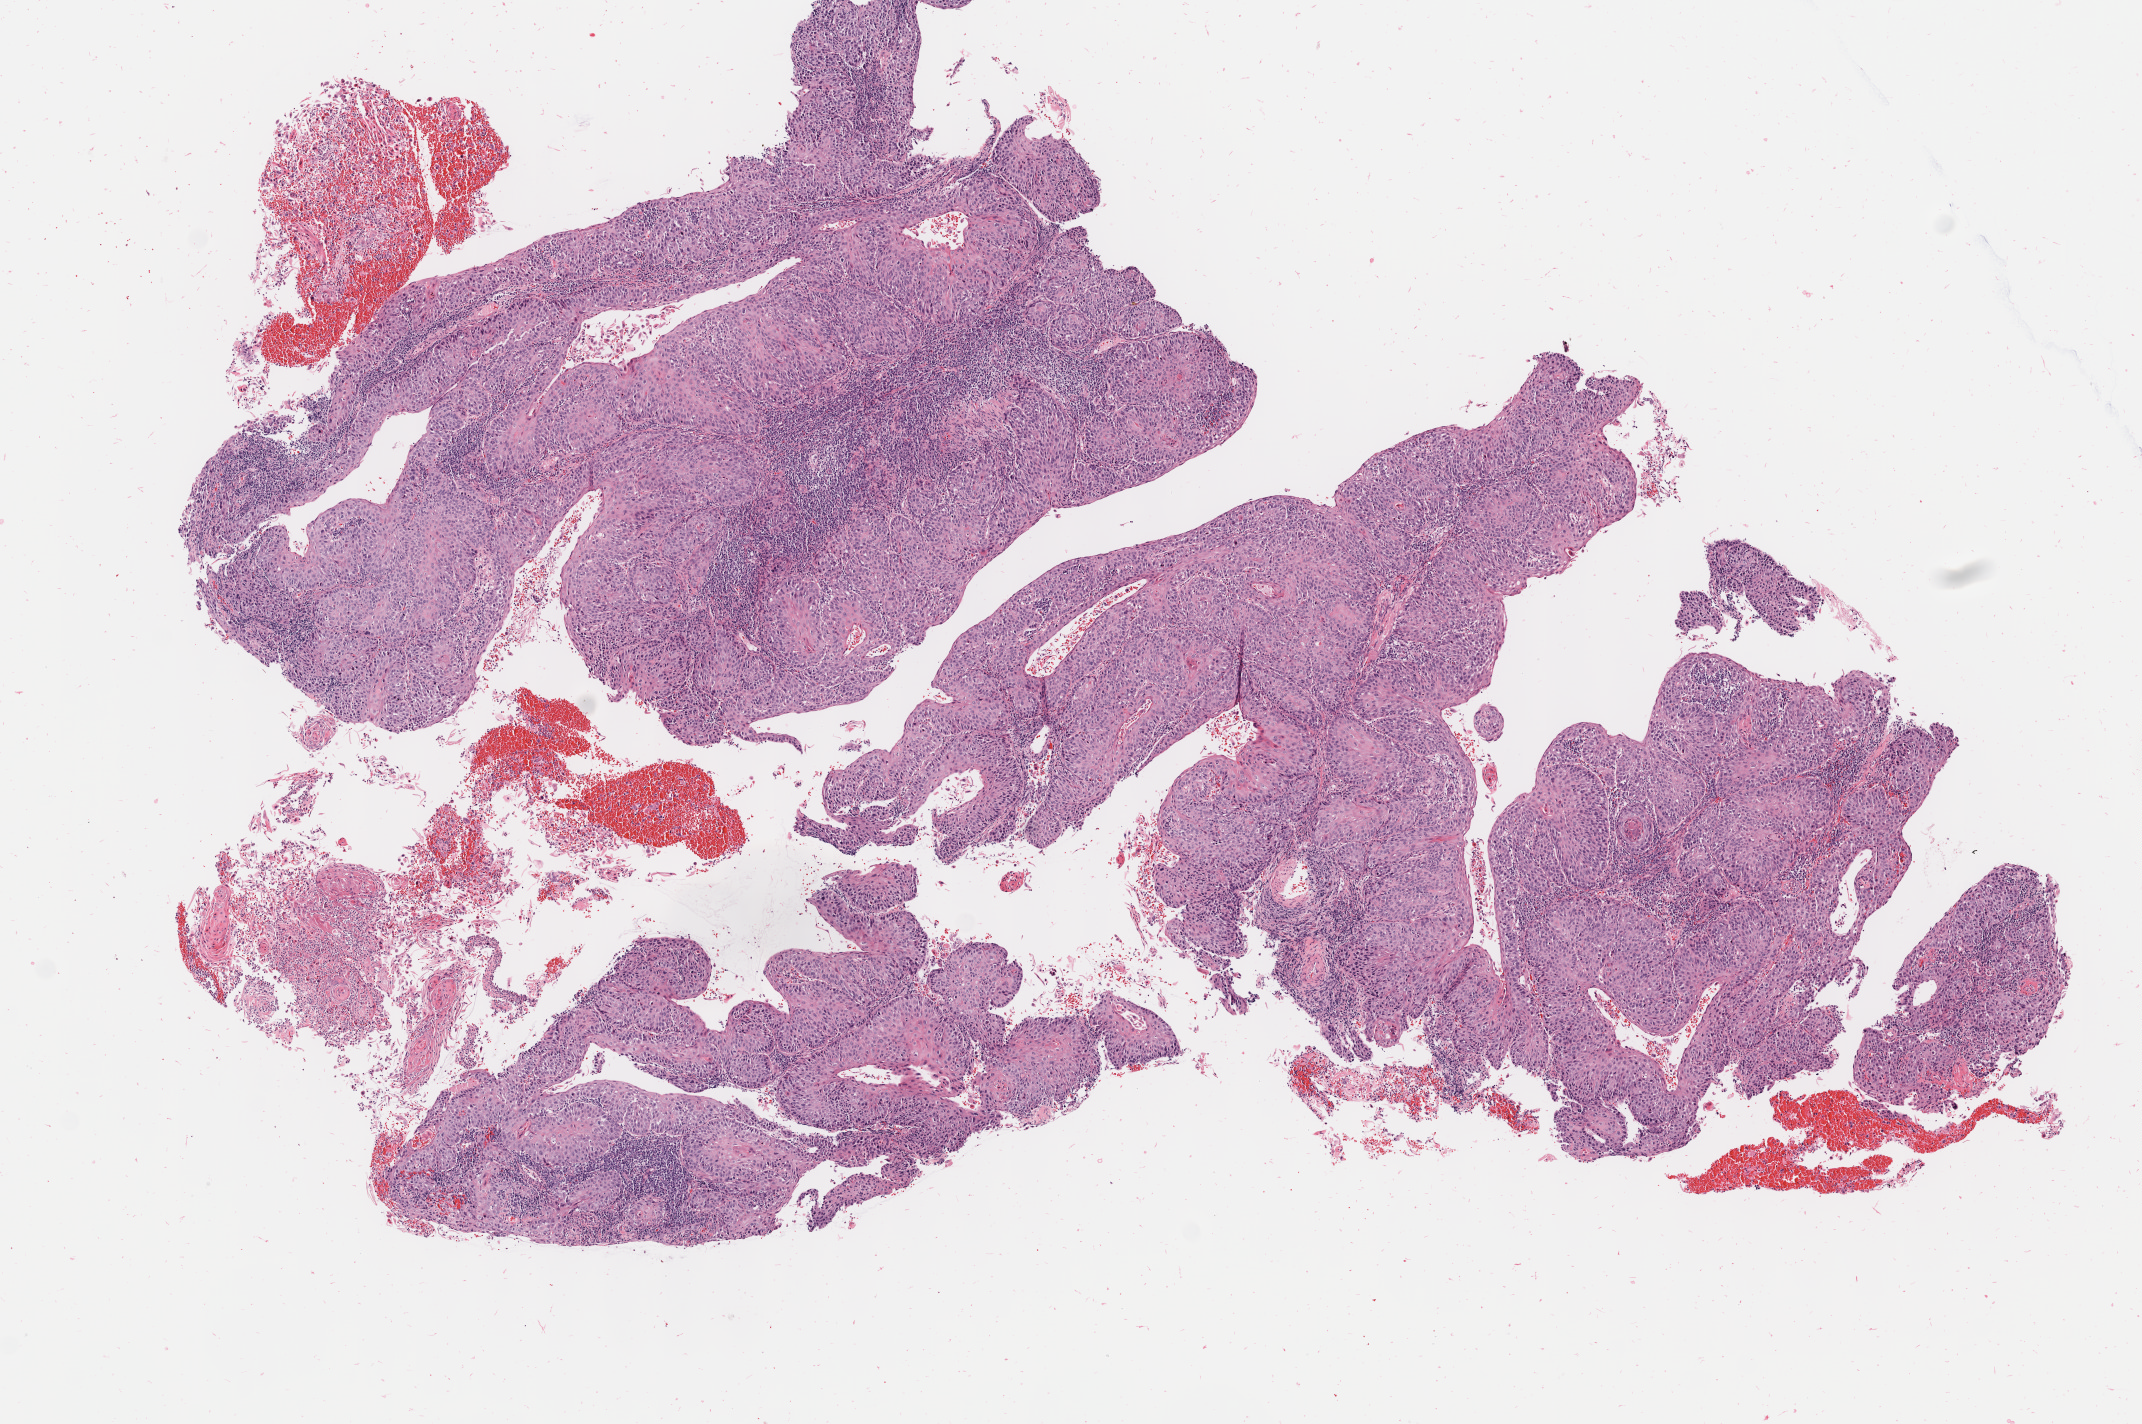
H&E whole-slide image, whole scanned area (about 8.5 x 5.7 mm) shown as a low-resolution overview. Tumor tissue. Site: cervix. Patient female; age 41 years.
Diagnosis: Squamous cell carcinoma, keratinizing, NOS.